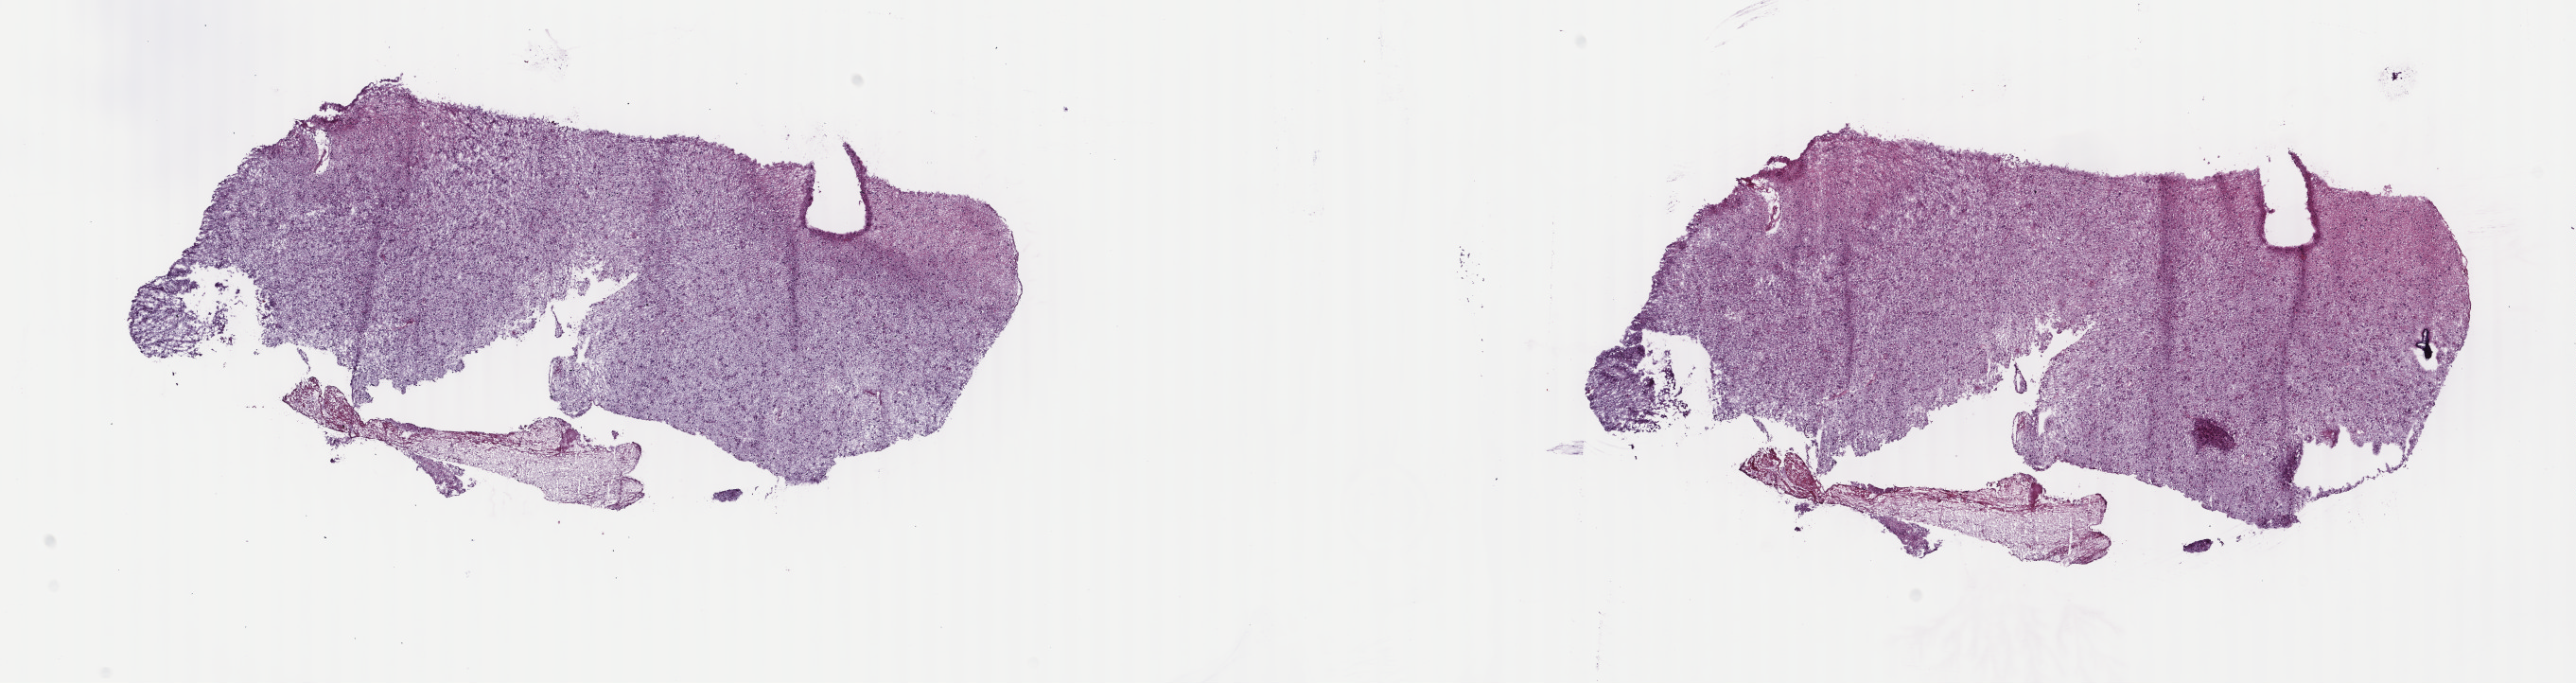
Digitized H&E-stained tissue section (whole slide) — low-resolution overview of the scanned area, about 21.7 x 5.7 mm; frozen section; primary tumour sample from the brain. Male patient; age at initial diagnosis 63 years. Histologic grade: G3 (poorly differentiated). Pathologist review of this section (percent, as recorded): tumour cells 80%, tumour nuclei 90%, normal cells 15%, stromal cells 0%, necrosis 5%. Infiltration values recorded for this section: lymphocyte infiltration 0%, monocyte infiltration 0%, neutrophil infiltration 0%.
Diagnosis: Mixed glioma (frontal lobe).